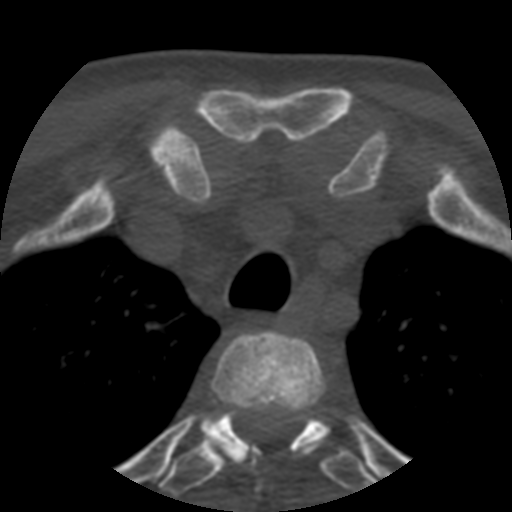
CT including the spine, one axial slice. Position 423 of 508 along the scan axis. Reconstruction kernel STANDARD. 120 kVp. Bone window (W 1800 / L 400 HU). 512 × 512 image matrix. Patient age 57 years. Case-level facts recorded for this patient, not image findings: primary cancer: prostate.
Annotated regions visible in this slice (semi-automatically segmented with operator editing):
- T2 vertebra: bounding box [x1, y1, x2, y2] px = [201, 331, 325, 461]
- T3 vertebra: [160, 411, 376, 496]